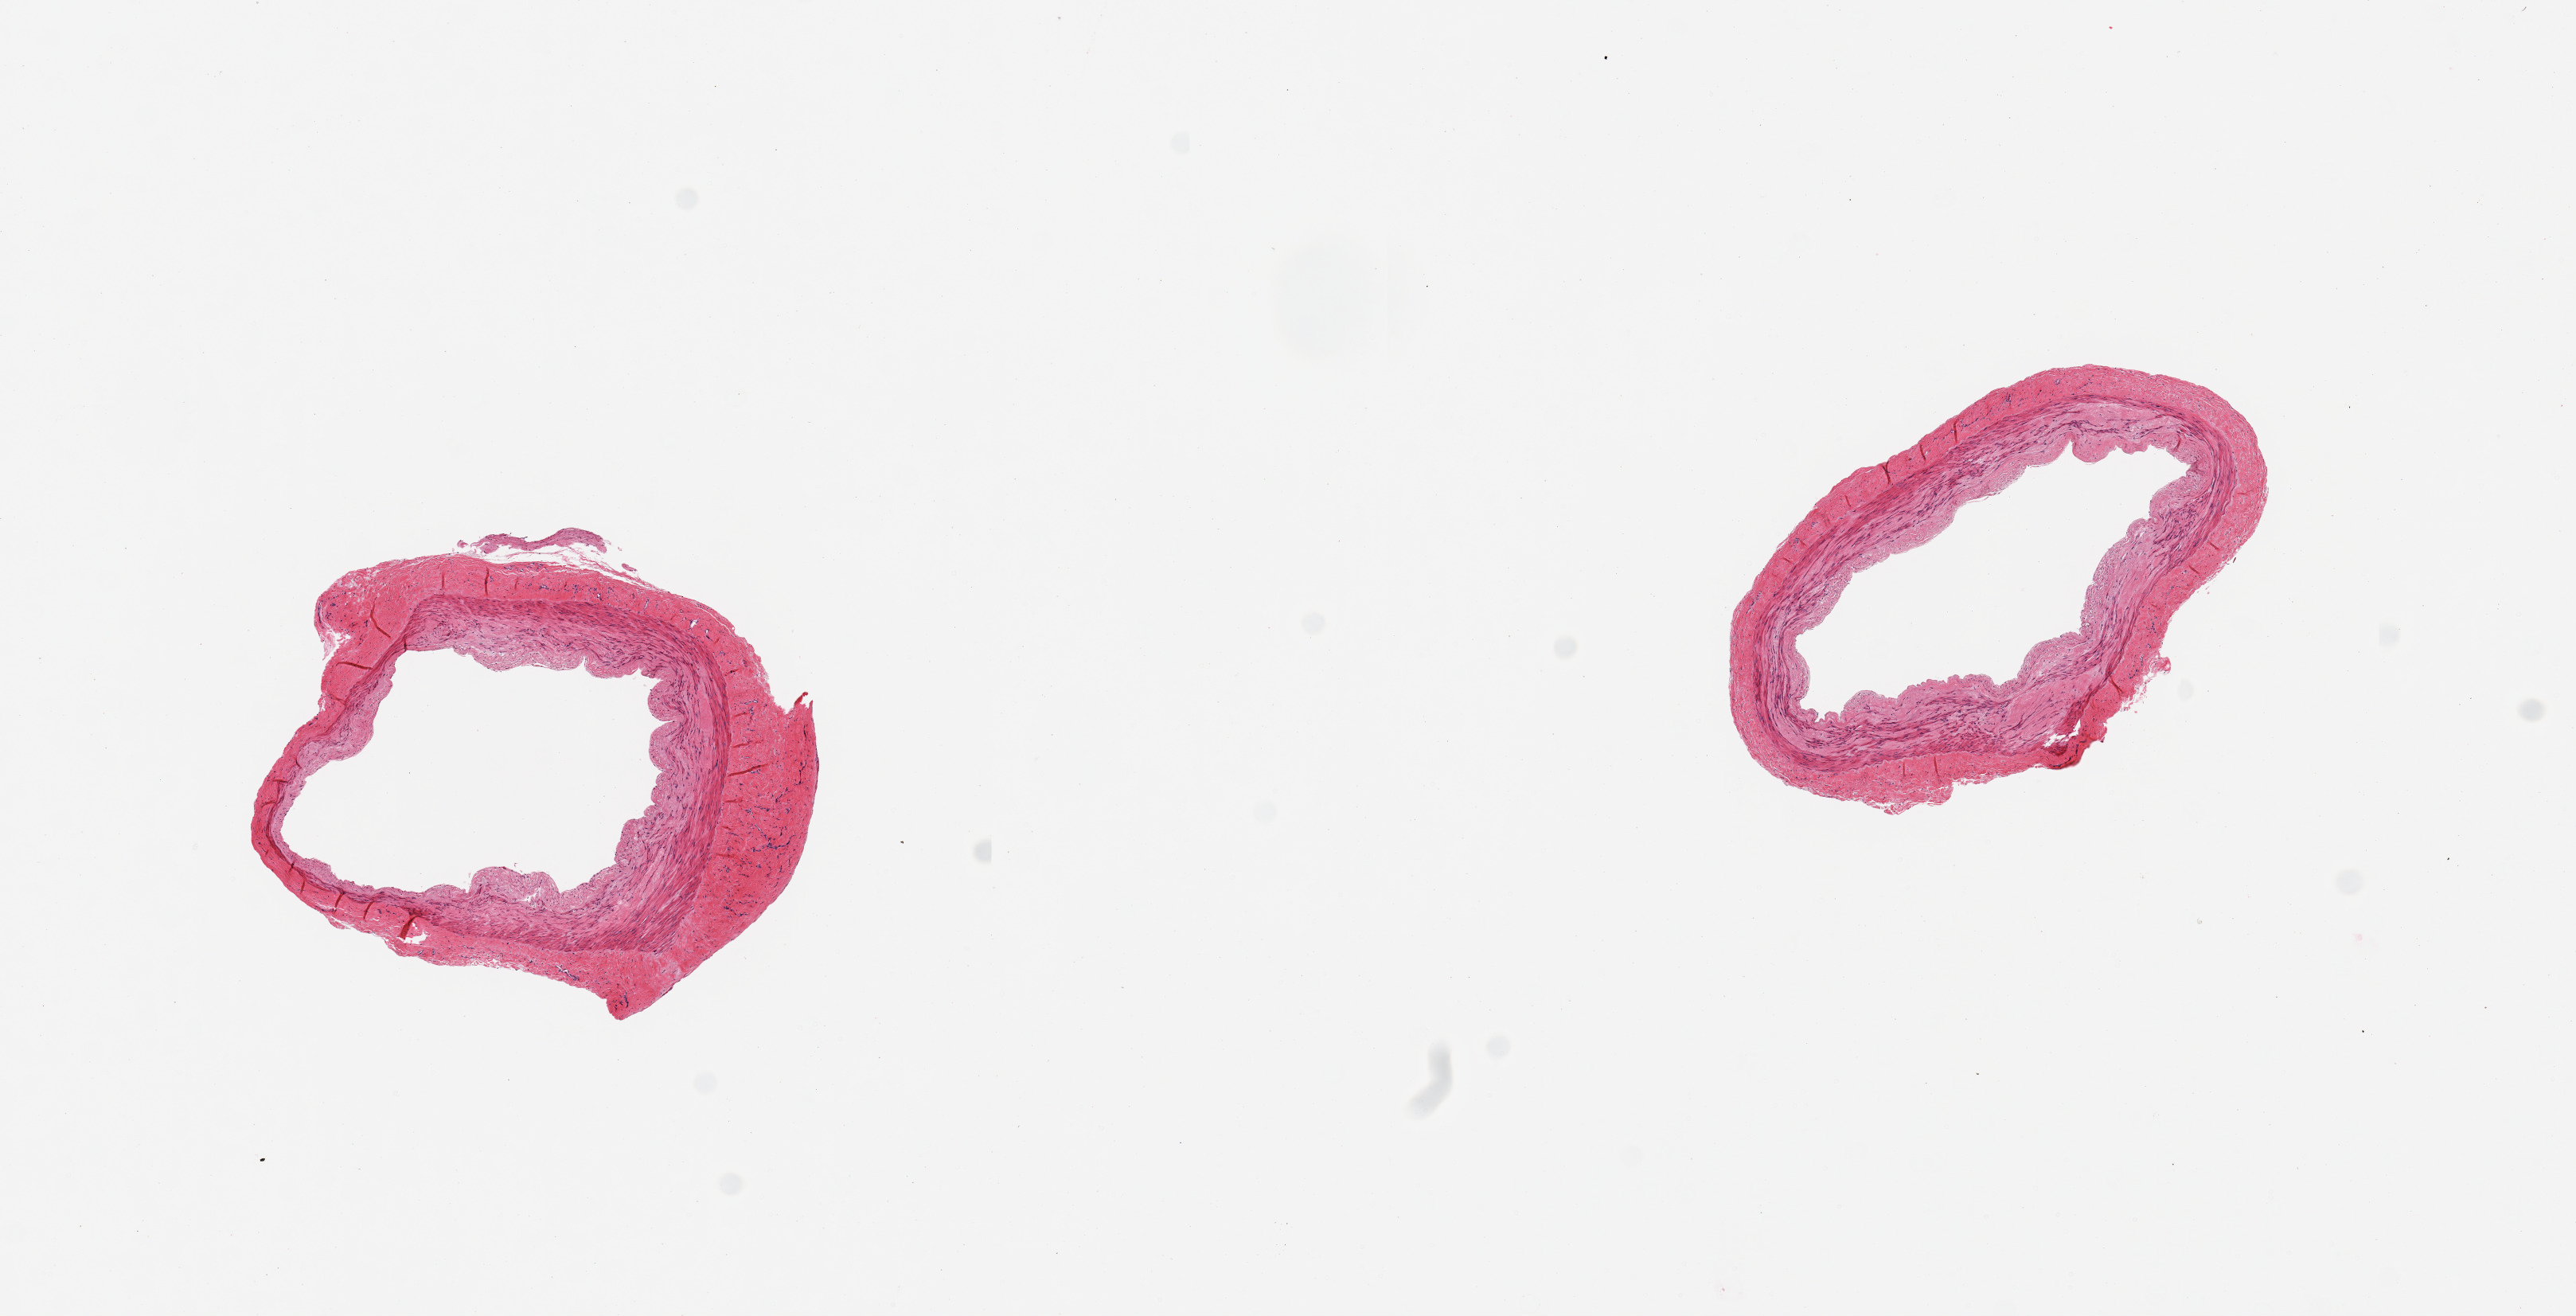
Digitized haematoxylin and eosin-stained section — low-resolution overview of the scanned area, about 12.8 x 6.5 mm (from a 20x scan), PAXgene-fixed paraffin-embedded (PFPE) section, sampled site (target tissue): tibial artery, tissue donor sample.
Pathologist's review note for this sample: 2 pieces; arteriosclerosis.